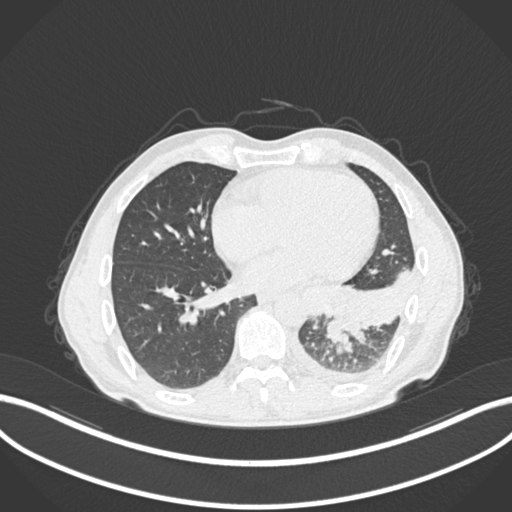
Chest CT, one axial slice; position 92 of 222 along the scan axis; 120 kVp; lung window (W 1500 / L -600 HU); 512 × 512 image matrix, field of view 400 × 400 mm. Male patient, age 47 years. Case-level facts recorded for this patient, not image findings: clinical TNM (as recorded): T3 N1 M1c.
Outlined on this slice (bounding box drawn by a radiologist):
- lung tumour (recorded histology: small cell carcinoma): bounding box (x1, y1, x2, y2) in pixels: (320, 314, 353, 346)